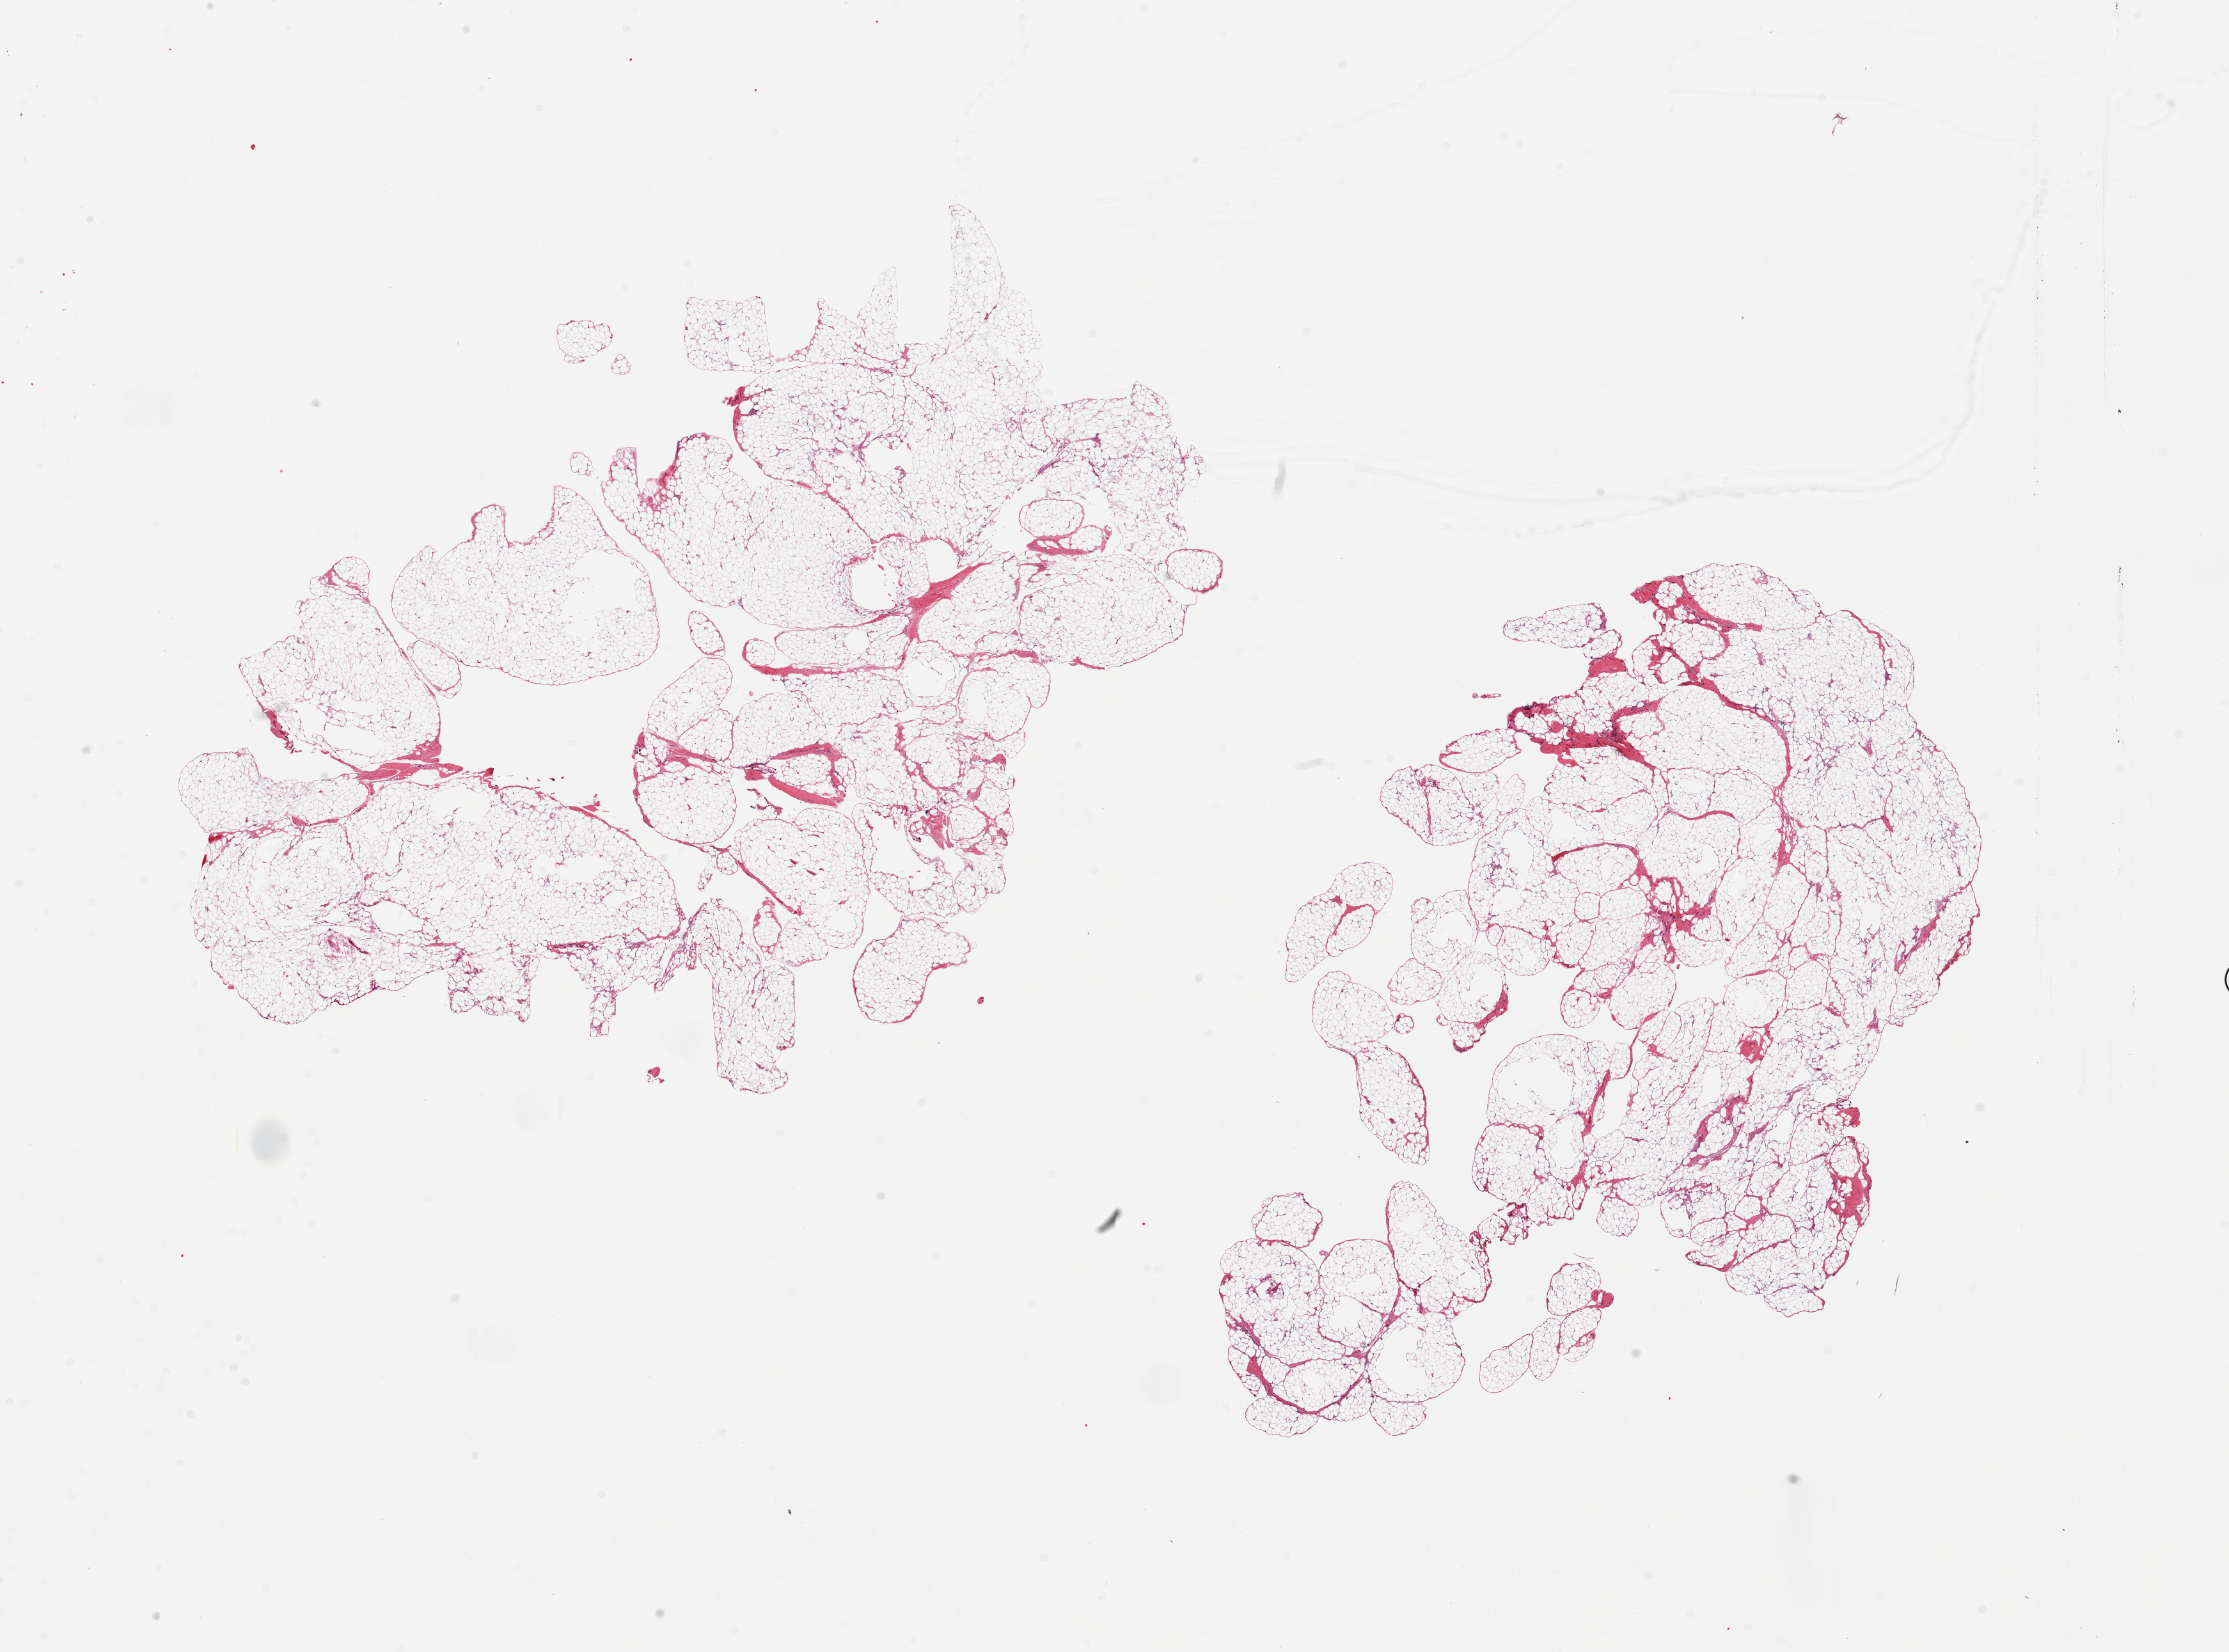
Whole-slide image, H&E stain, shown as a low-resolution overview of the whole scanned area (about 27.6 x 20.4 mm); PAXgene-fixed paraffin-embedded (PFPE) section; target tissue: omentum; donor tissue sample.
Pathologist's review note for this sample: 2 pieces, minimal fascial/vasuclar tissue.